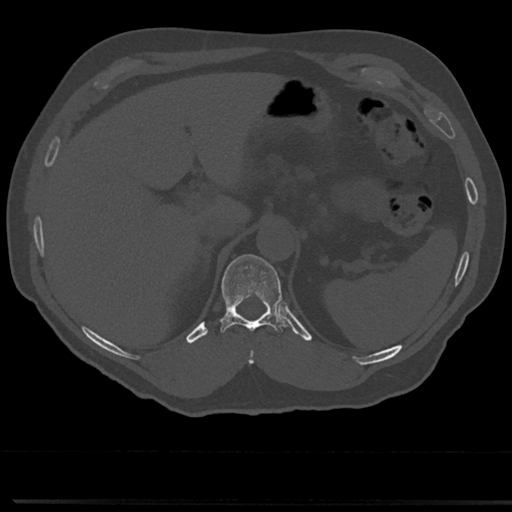
CT including the spine, one axial slice. 120 kVp. Bone window (W 1800 / L 400 HU). 512 × 512 image matrix, field of view 355 × 355 mm. Patient: male, 61 years. Case-level facts recorded for this patient, not image findings: primary cancer: prostate.
Annotated regions visible in this slice (semi-automatically segmented with operator editing):
- T10 vertebra: bounding box [x1, y1, x2, y2] px = [246, 347, 256, 365]
- T11 vertebra: [214, 255, 289, 335]